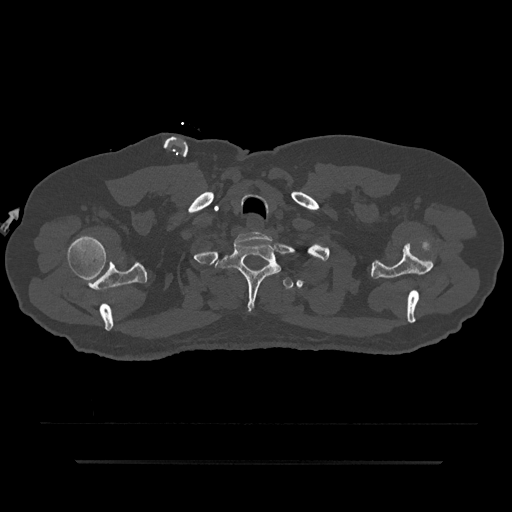
CT including the spine, one axial slice; slice 736 of 797 in the series (ordered by position); reconstruction kernel Br40s/3; 120 kVp; bone window (W 1800 / L 400 HU); 0.5 mm slice thickness; 512 × 512 image matrix, field of view 464 × 464 mm. Patient: male, 59 years. From the clinical record (not read from this slice): primary cancer: bile ducts.
Outlined on this slice (semi-automatically segmented with operator editing):
- T1 vertebra: box from (x=215, y=239) to (x=281, y=311) px
- T2 vertebra: (x=282, y=278)–(x=294, y=289)